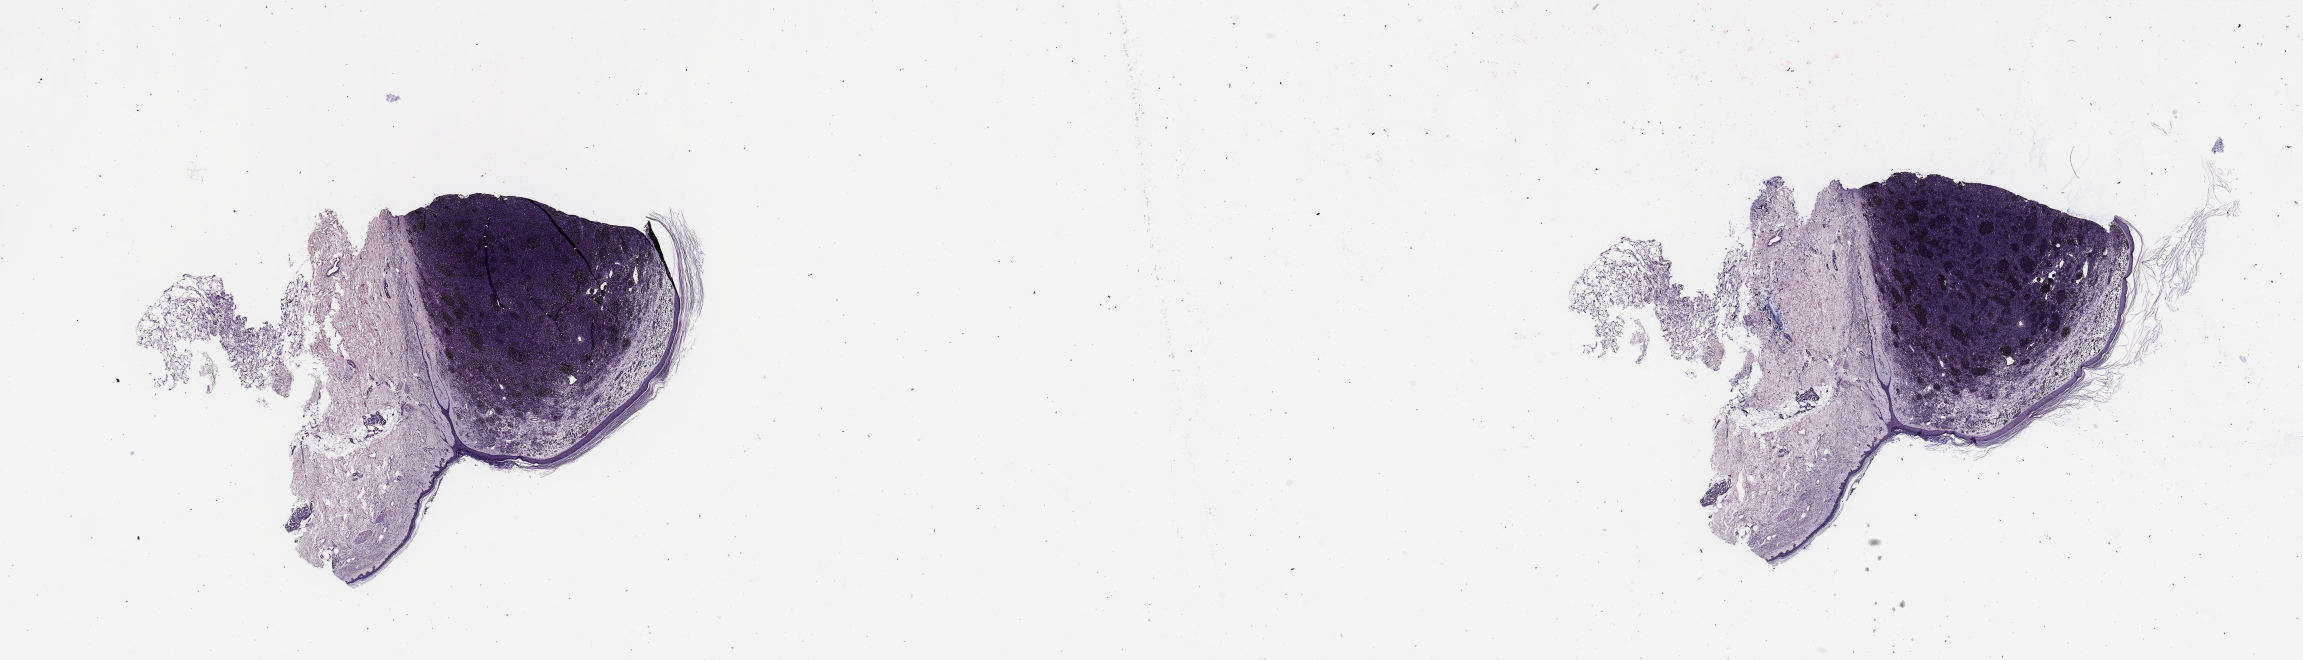
Hematoxylin and eosin (H&E) stained whole-slide image, shown as a low-resolution overview of the whole scanned area (about 36.4 x 10.4 mm, acquisition: 20x scan), melanoma tumour tissue; sampled site not recorded. 78-year-old female patient.
AJCC pathologic stage: IIB. Histologic diagnosis: Malignant melanoma, NOS. Primary tumour site (as recorded): extremities.